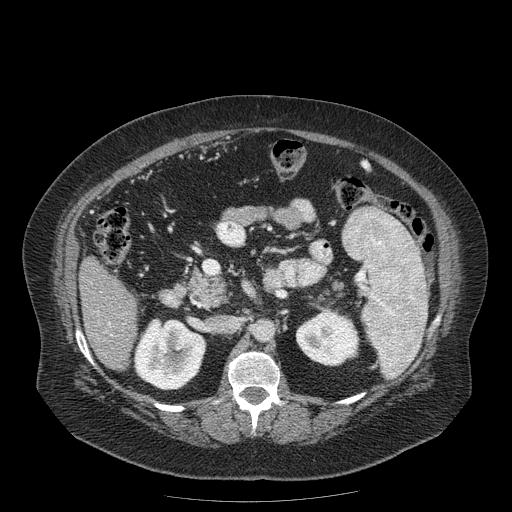
Contrast-enhanced abdominal CT (liver protocol), one axial slice; slice 69 of 204 in the series (ordered by position); reconstruction kernel STANDARD; 120 kVp; soft-tissue window (W 400 / L 40 HU); 2.5 mm slice thickness; 512 × 512 image matrix, field of view 440 × 440 mm. From the clinical record (not read from this slice): diagnosis: hepatocellular carcinoma (patient treated with transarterial chemoembolisation; whether this scan precedes or follows treatment is not stated here); TNM stage (as recorded): Stage-IIIB; Child-Pugh class: A; tumour nodularity: uninodular.
Structures marked on this image (semi-automatically segmented with operator editing):
- liver parenchyma outside the tumour (the mass and vessels are separate outlines, so this box may not span the whole liver): bounding box <78,256,136,370> (left, top, right, bottom; pixels)
- liver vessels: <108,322,111,325>